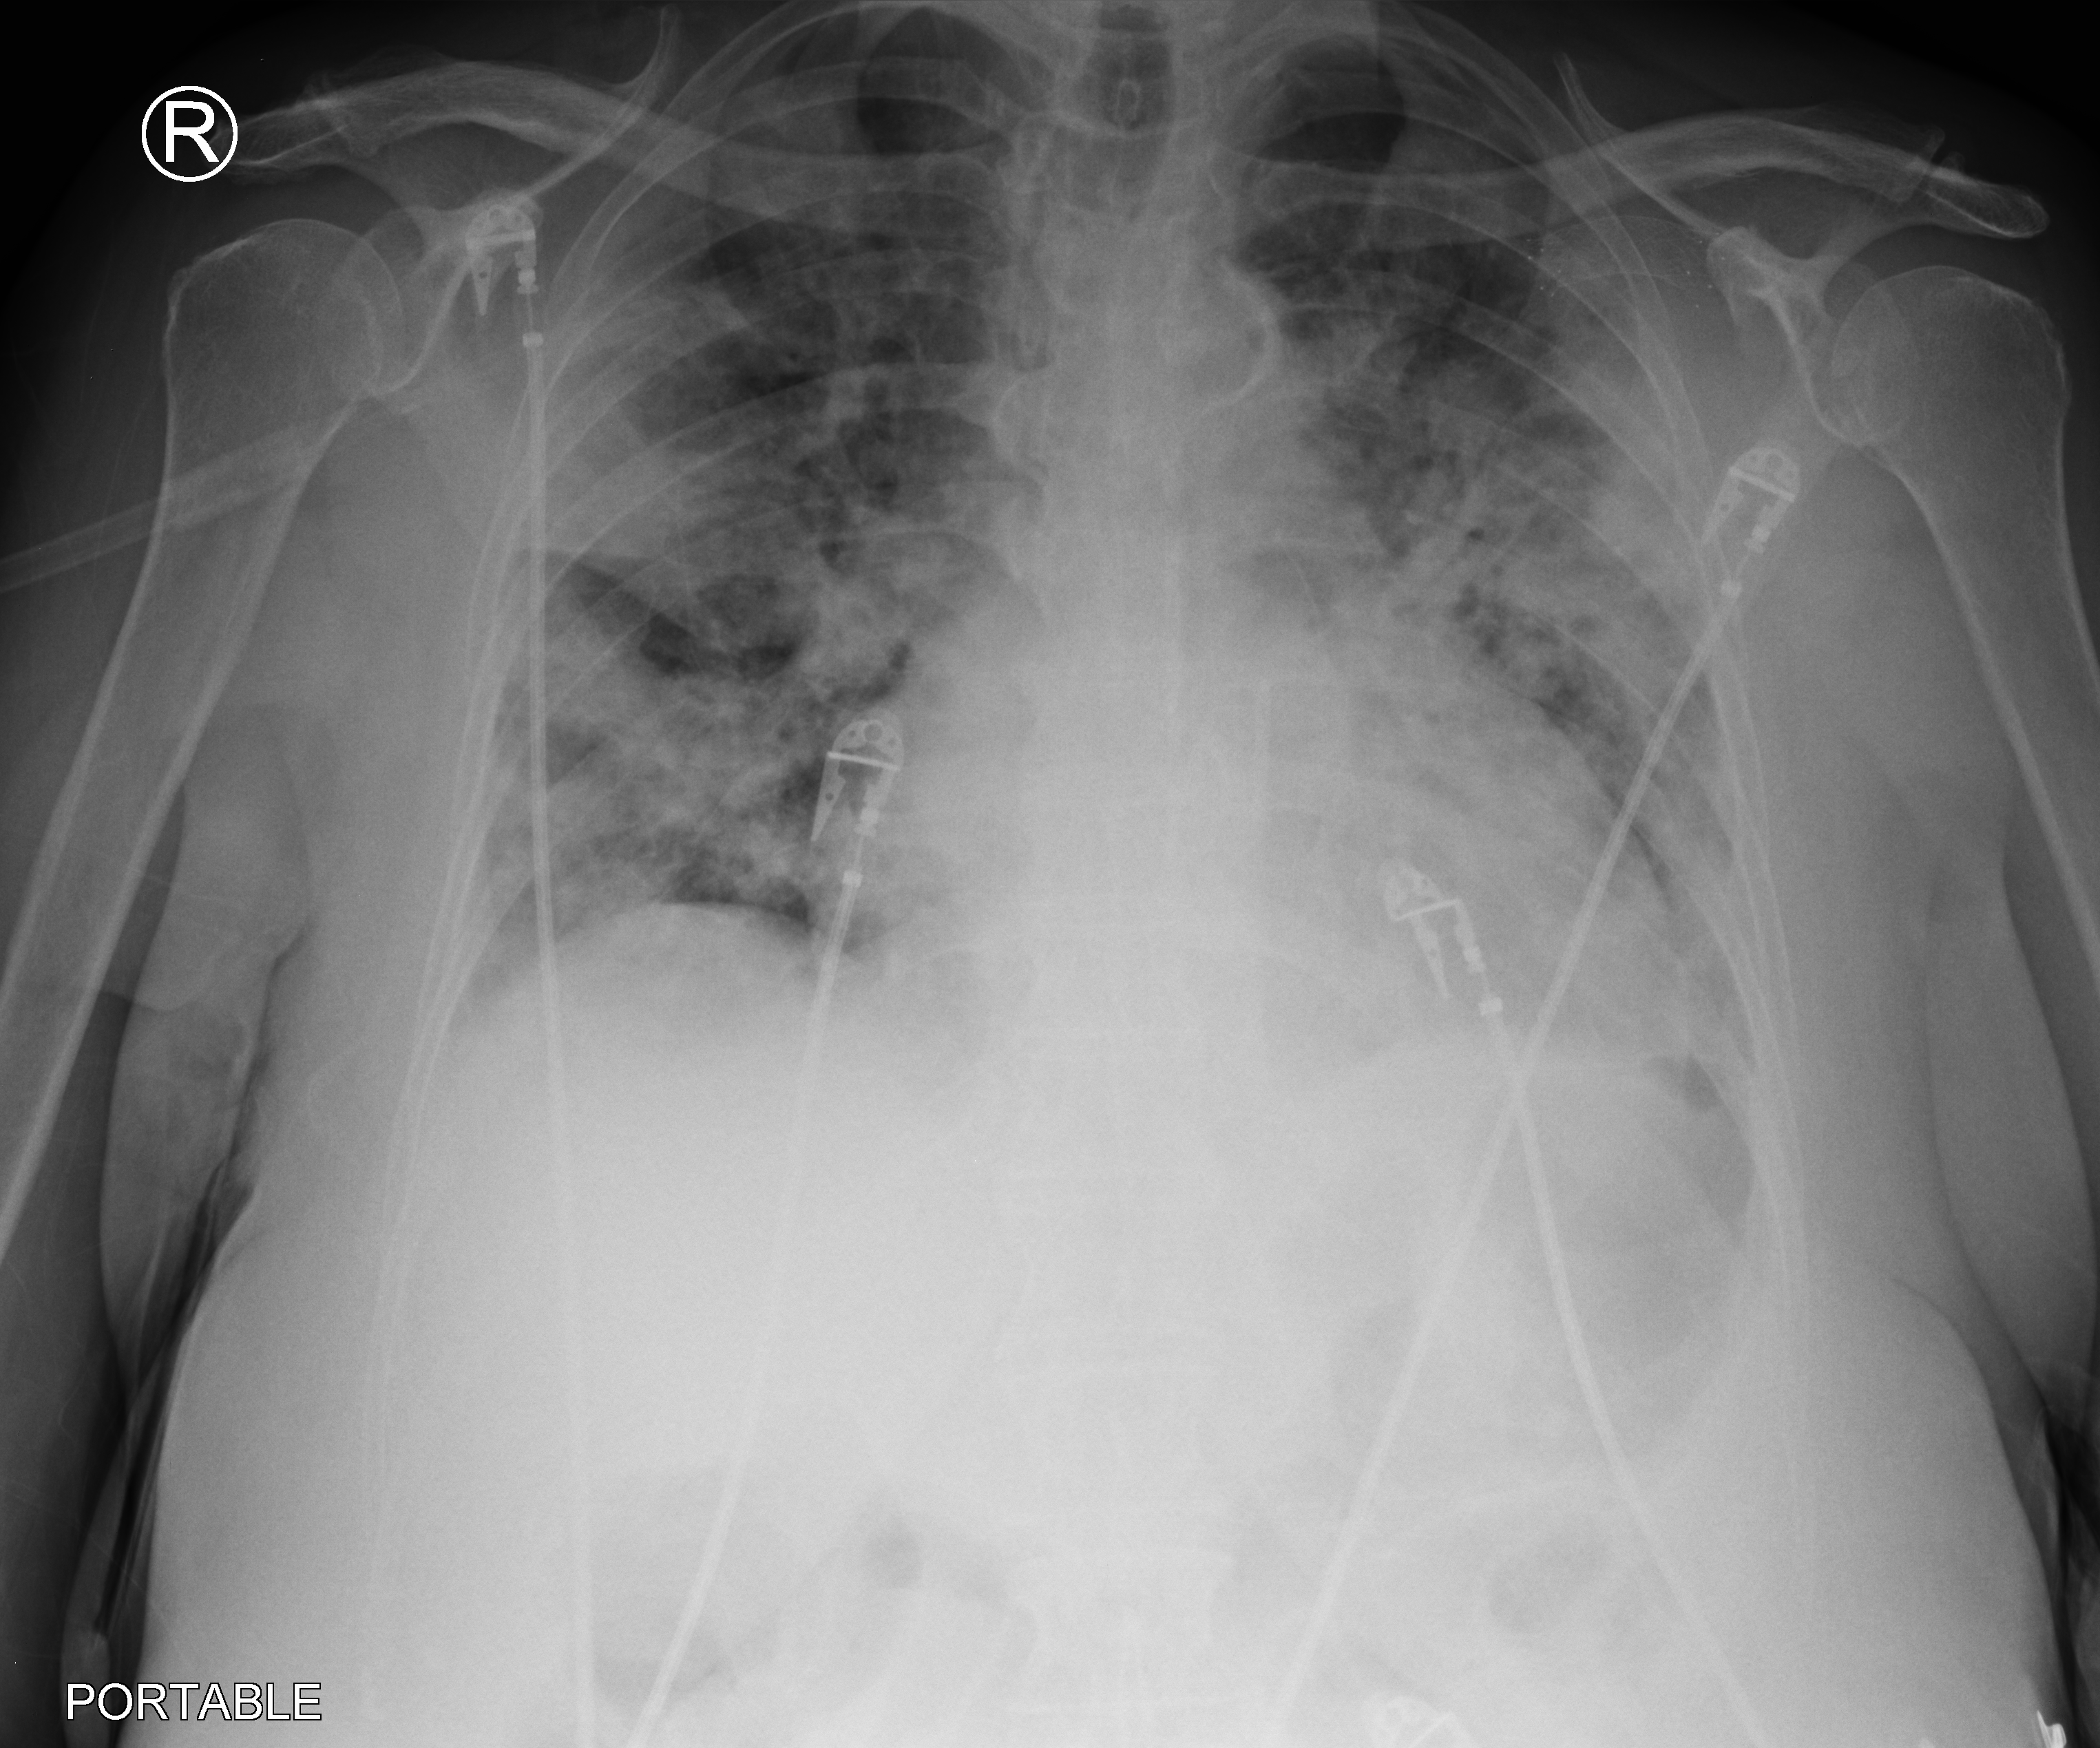
Chest X-ray (portable). Female patient hospitalised with COVID-19, age 60–74 years.
Hospital-stay facts (about this admission, not read from this image; timing relative to this image not recorded):
- admitted to intensive care during this hospital stay: yes
- mechanically ventilated during this hospital stay: yes